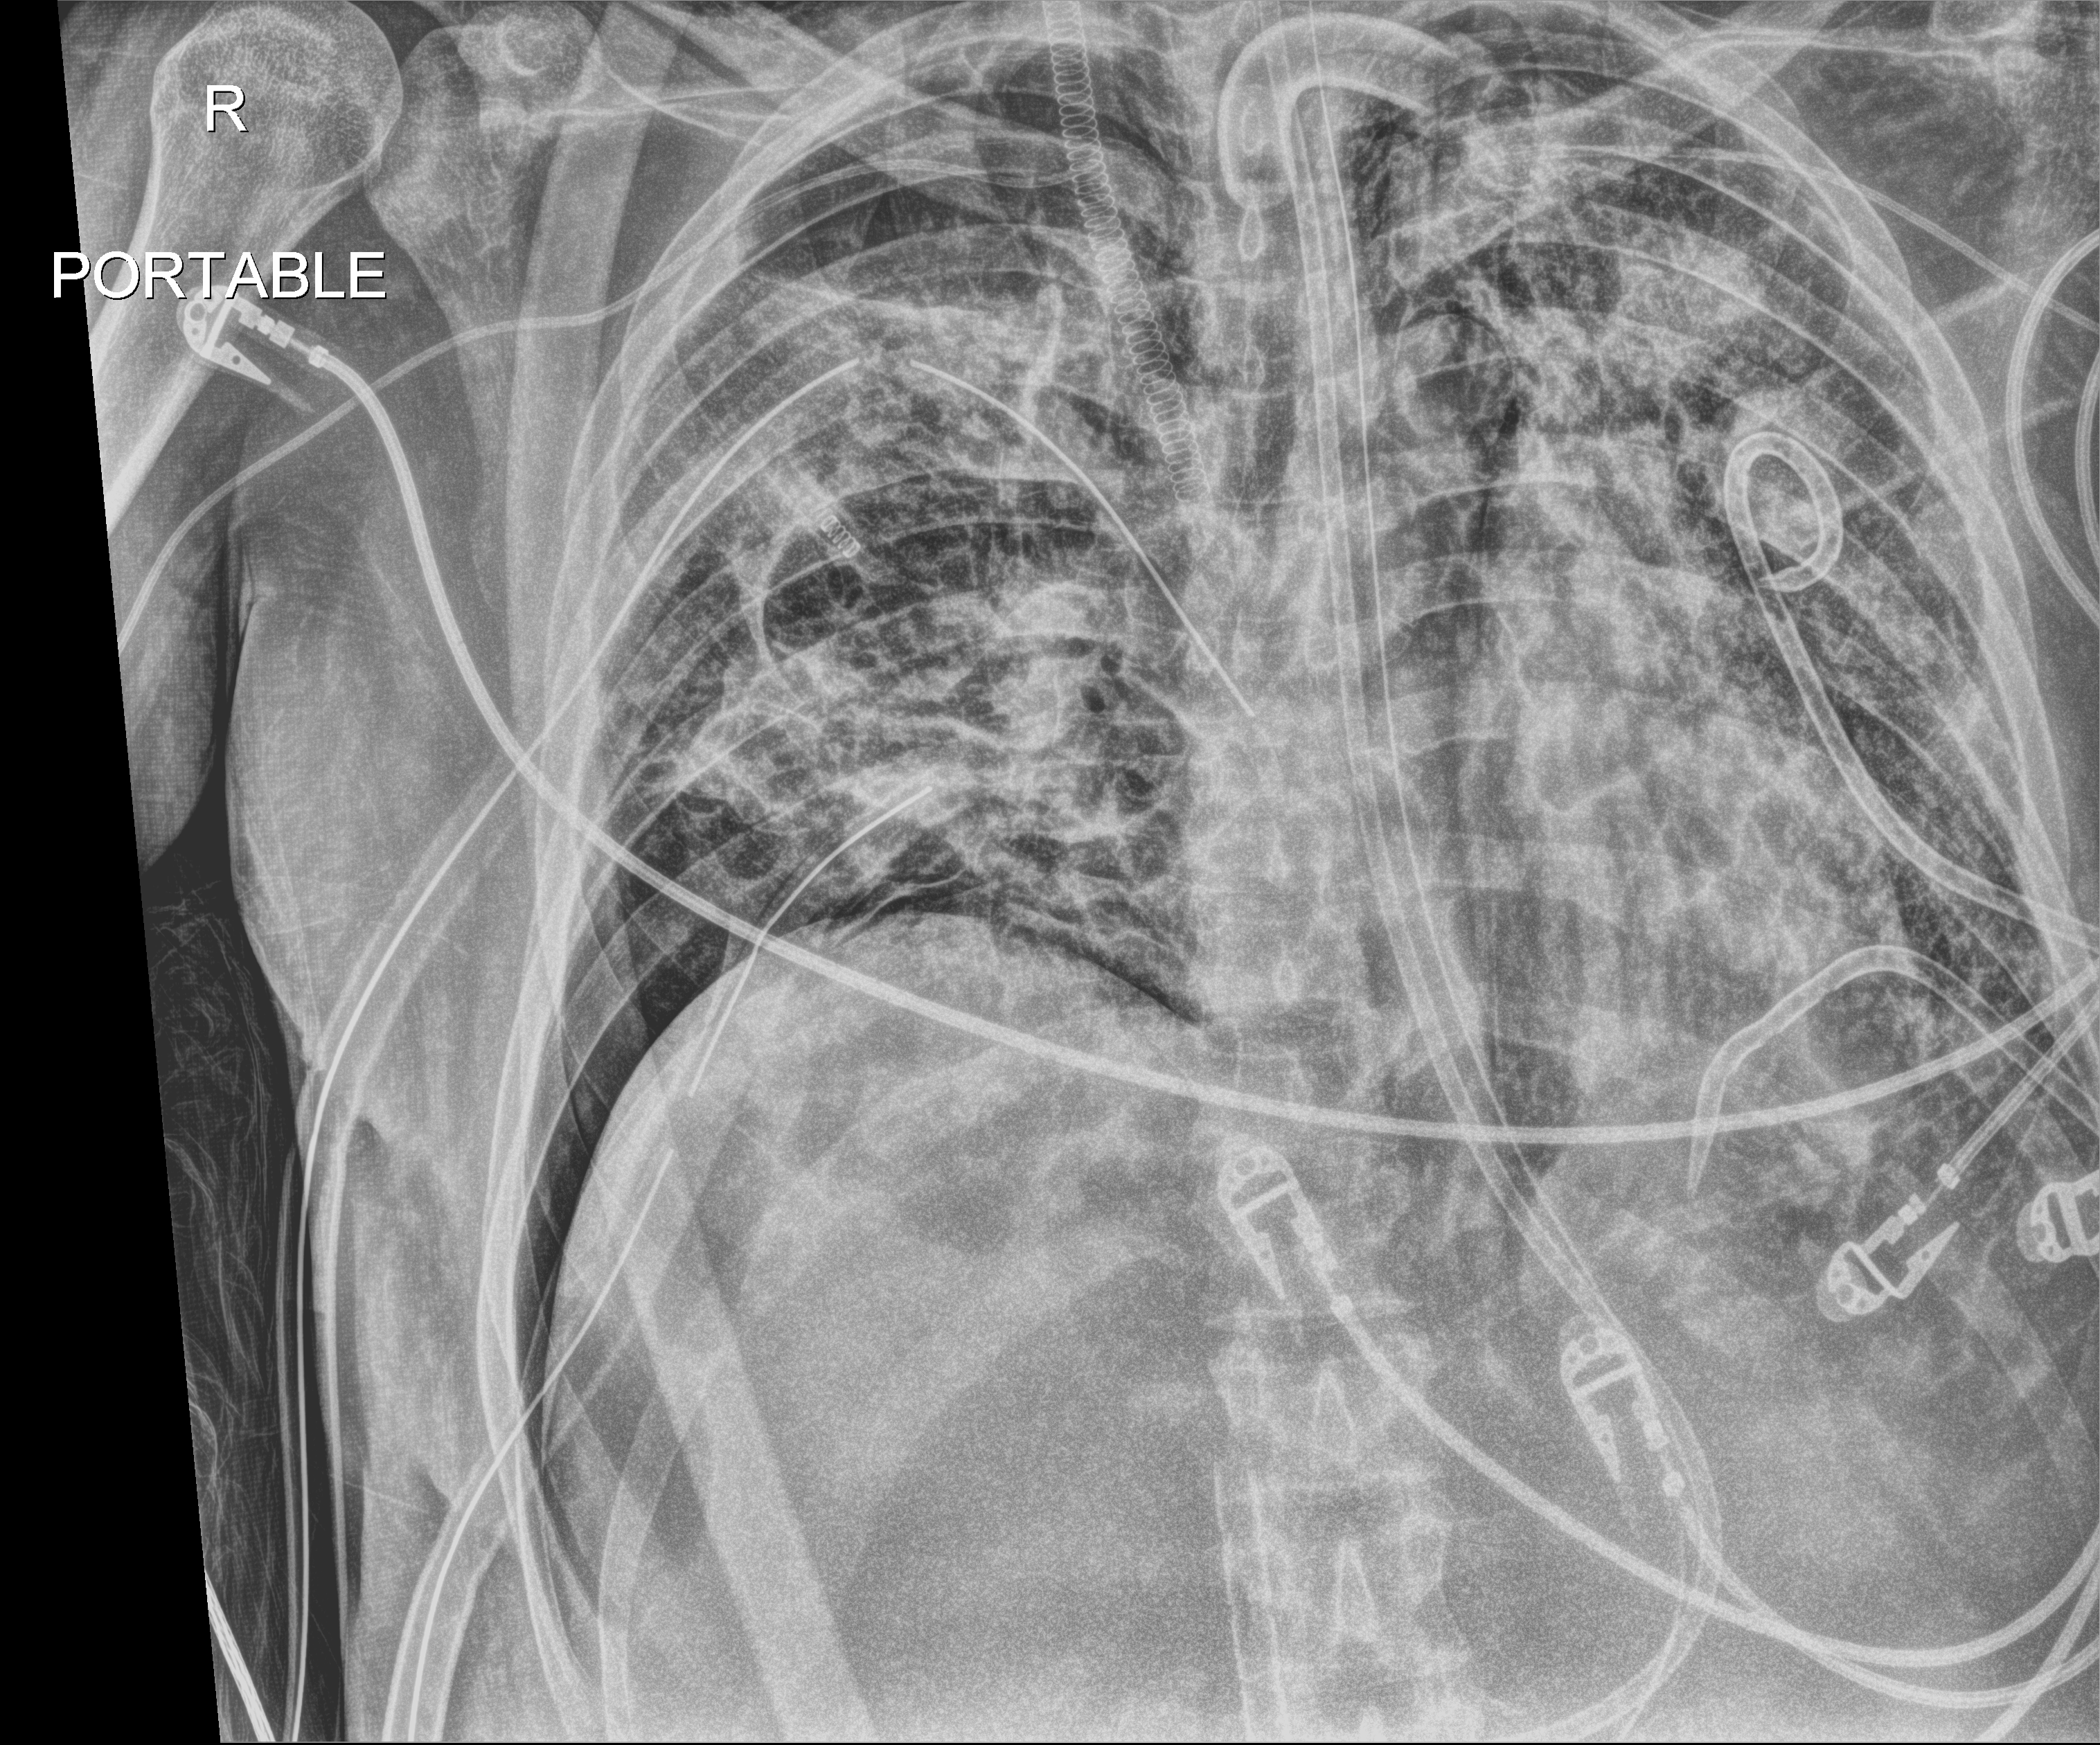
Chest radiograph (digital radiography); anteroposterior (AP) projection. Patient hospitalised with COVID-19, aged 18–59 years.
Admission-level facts for this patient (not findings on this image; timing relative to this image not recorded):
- admitted to intensive care during this hospital stay: yes
- mechanically ventilated during this hospital stay: yes